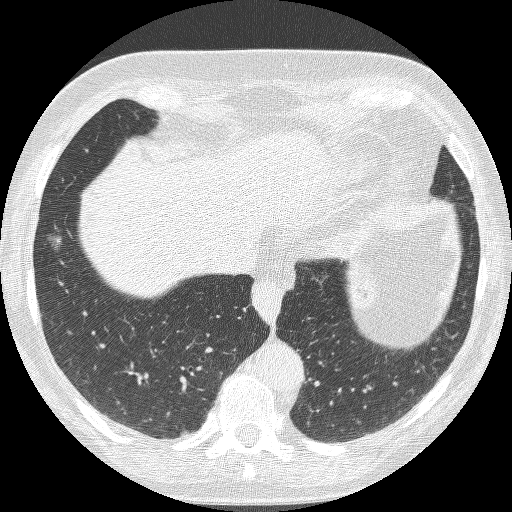
Axial slice from a low-dose chest CT screening exam. Baseline annual screen. Lung window (W 1500 / L -600 HU). 1.25 mm slice thickness. 512 × 512 image matrix. Female, age 68 years at enrolment. Current smoker at enrolment.
Lesion marked by an expert reader, bounding box (x1, y1, x2, y2) in pixels: (35, 215, 87, 262). Screening reader's record for this exam (one nodule recorded; not confirmed to be the boxed lesion): non-calcified nodule or mass ≥4 mm, right lower lobe, 16 × 12 mm, poorly defined margins, ground glass attenuation. Later outcome: lung cancer diagnosed 406 days after this screen — bronchiolo-alveolar adenocarcinoma, NOS, right lower lobe, well differentiated (G1), stage IA (AJCC 6th edition), 13 mm at pathology.